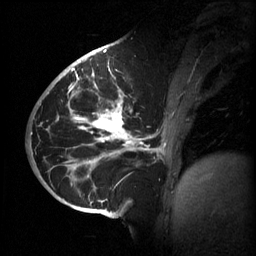
Breast MRI (dynamic contrast-enhanced), one sagittal slice. Position 27 of 60 along the scan axis. 3 images stored at this slice position (order not interpretable as contrast timing). 1.5 T. TE 4.2 ms, TR 11 ms. 2 mm slice thickness. 256 × 256 image matrix. Patient: female, 51 years.
Annotated regions visible in this slice (semi-automatic segmentation, software-assisted and operator-edited):
- analysis volume of interest (the breast-tissue region the enhancement analysis was run in; not a lesion): bounding box [x1, y1, x2, y2] px = [63, 80, 187, 201]
- tumour enhancement mask (voxels above the 70 % enhancement threshold inside the analysis volume of interest): [67, 80, 165, 201]